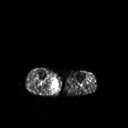
FDG PET of an extremity soft-tissue mass (from a PET/CT study), one axial slice. Position 146 of 267 along the scan axis. 3.27 mm slice thickness. 128 × 128 image matrix, field of view 500 × 500 mm. Male patient, age 69 years. Case-level facts recorded for this patient, not image findings: histological type: pleiomorphic liposarcoma; grade: high; site of the primary tumour: right calf.
Outlined on this slice (expert contour drawn on MRI and transferred to this co-registered scan by the dataset authors):
- gross tumour volume including surrounding oedema: bounding box [x1, y1, x2, y2] px = [53, 78, 58, 88]